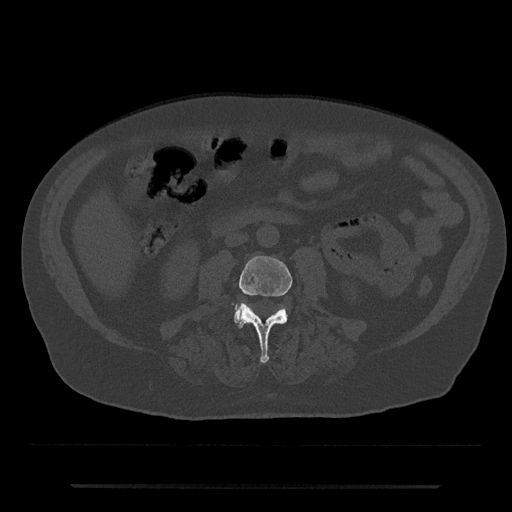
CT including the spine, one axial slice. Position 399 of 797 along the scan axis. Reconstruction kernel Br40s/3. 120 kVp. Bone window (W 1800 / L 400 HU). 512 × 512 image matrix, field of view 434 × 434 mm. Male patient, age 80 years. From the clinical record (not read from this slice): primary cancer: prostate; vertebrae with lytic lesions (as recorded): L1, T11.
Structures marked on this image (semi-automatic segmentation, software-assisted and operator-edited):
- L3 vertebra: bounding box [x1, y1, x2, y2] px = [239, 256, 293, 363]
- L4 vertebra: [234, 306, 288, 323]